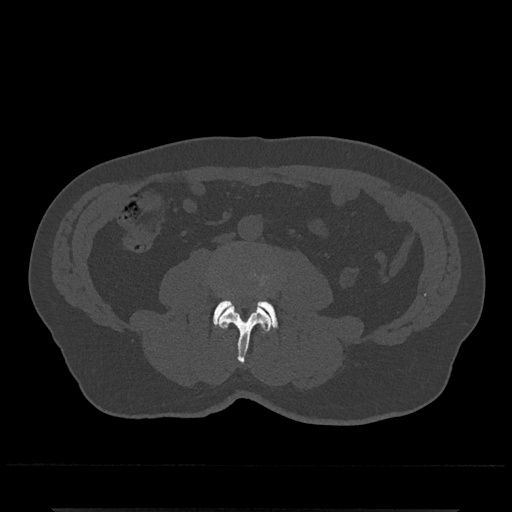
CT including the spine, one axial slice. Slice 195 of 797 in the series (ordered by position). Reconstruction kernel Br40s/3. Bone window (W 1800 / L 400 HU). 512 × 512 image matrix. Male patient, age 67 years. Case-level facts recorded for this patient, not image findings: primary cancer: prostate.
Outlined on this slice (semi-automatically segmented with operator editing):
- L3 vertebra: box from (x=218, y=275) to (x=272, y=364) px
- L4 vertebra: (x=213, y=299)–(x=278, y=328)